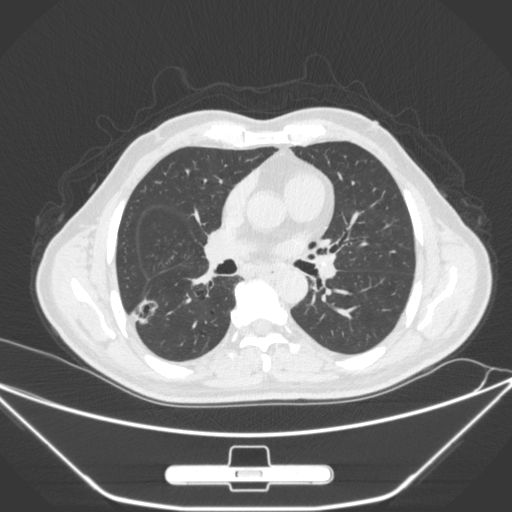
Chest CT, one axial slice. Slice 154 of 310 in the series (ordered by position). Lung window (W 1500 / L -600 HU). 1 mm slice thickness. 512 × 512 image matrix, field of view 398 × 398 mm. Patient: male, 71 years. From the clinical record (not read from this slice): clinical TNM (as recorded): T1c N0 M0; histopathological grade: G2.
Annotated regions visible in this slice (bounding box drawn by a radiologist):
- lung tumour (recorded histology: adenocarcinoma): box from (x=134, y=296) to (x=167, y=332) px